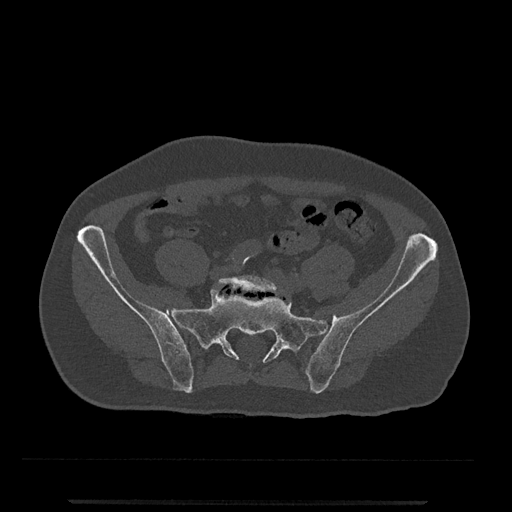
CT including the spine, one axial slice; slice 19 of 797 in the series (ordered by position); 120 kVp; bone window (W 1800 / L 400 HU); 512 × 512 image matrix. Patient: male, 63 years. Case-level facts recorded for this patient, not image findings: primary cancer: prostate.
Outlined on this slice (semi-automatic segmentation, software-assisted and operator-edited):
- L5 vertebra: box from (x=217, y=275) to (x=279, y=293) px